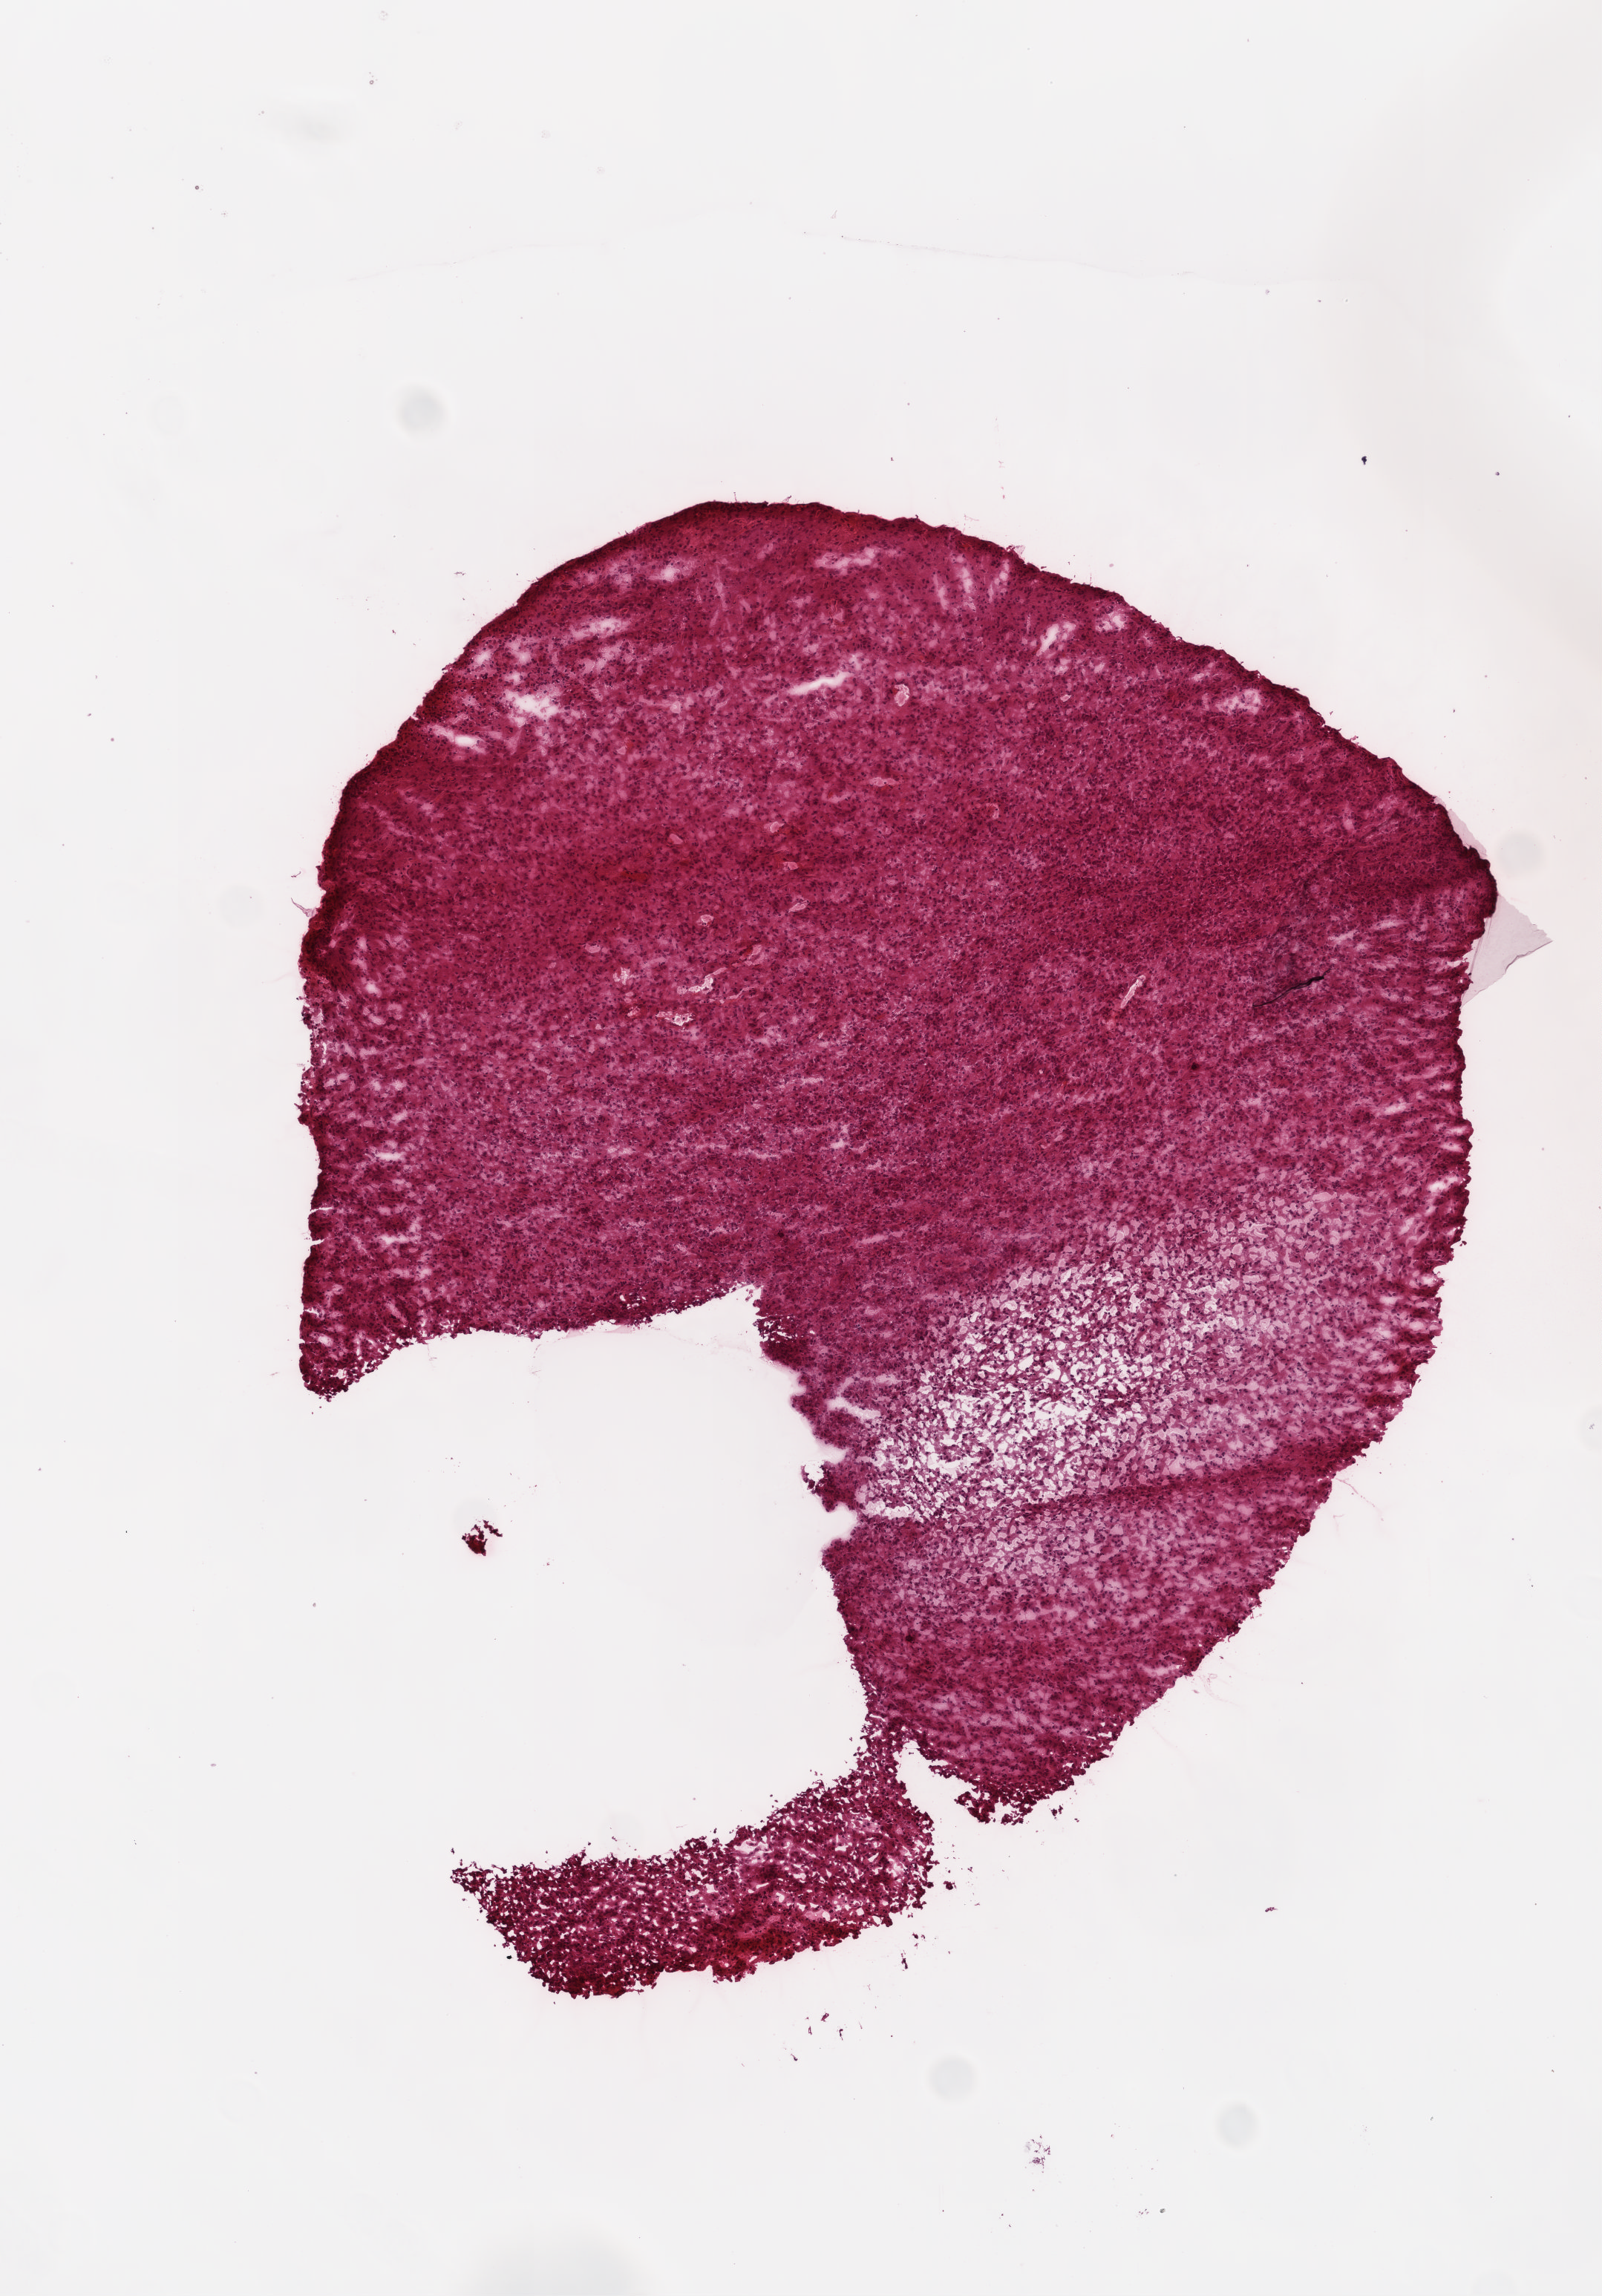
Whole-slide histology image, H&E, shown as a low-resolution overview of the whole scanned area (about 4.4 x 6.2 mm, slide scanned at 20x); frozen section; primary tumour sample from the brain. Patient: female, age at initial diagnosis 48 years. Composition of this section per pathologist review: tumour cells 100%, tumour nuclei 100%, normal cells 0%, stromal cells 0%, necrosis 0%.
- diagnosis: Glioblastoma